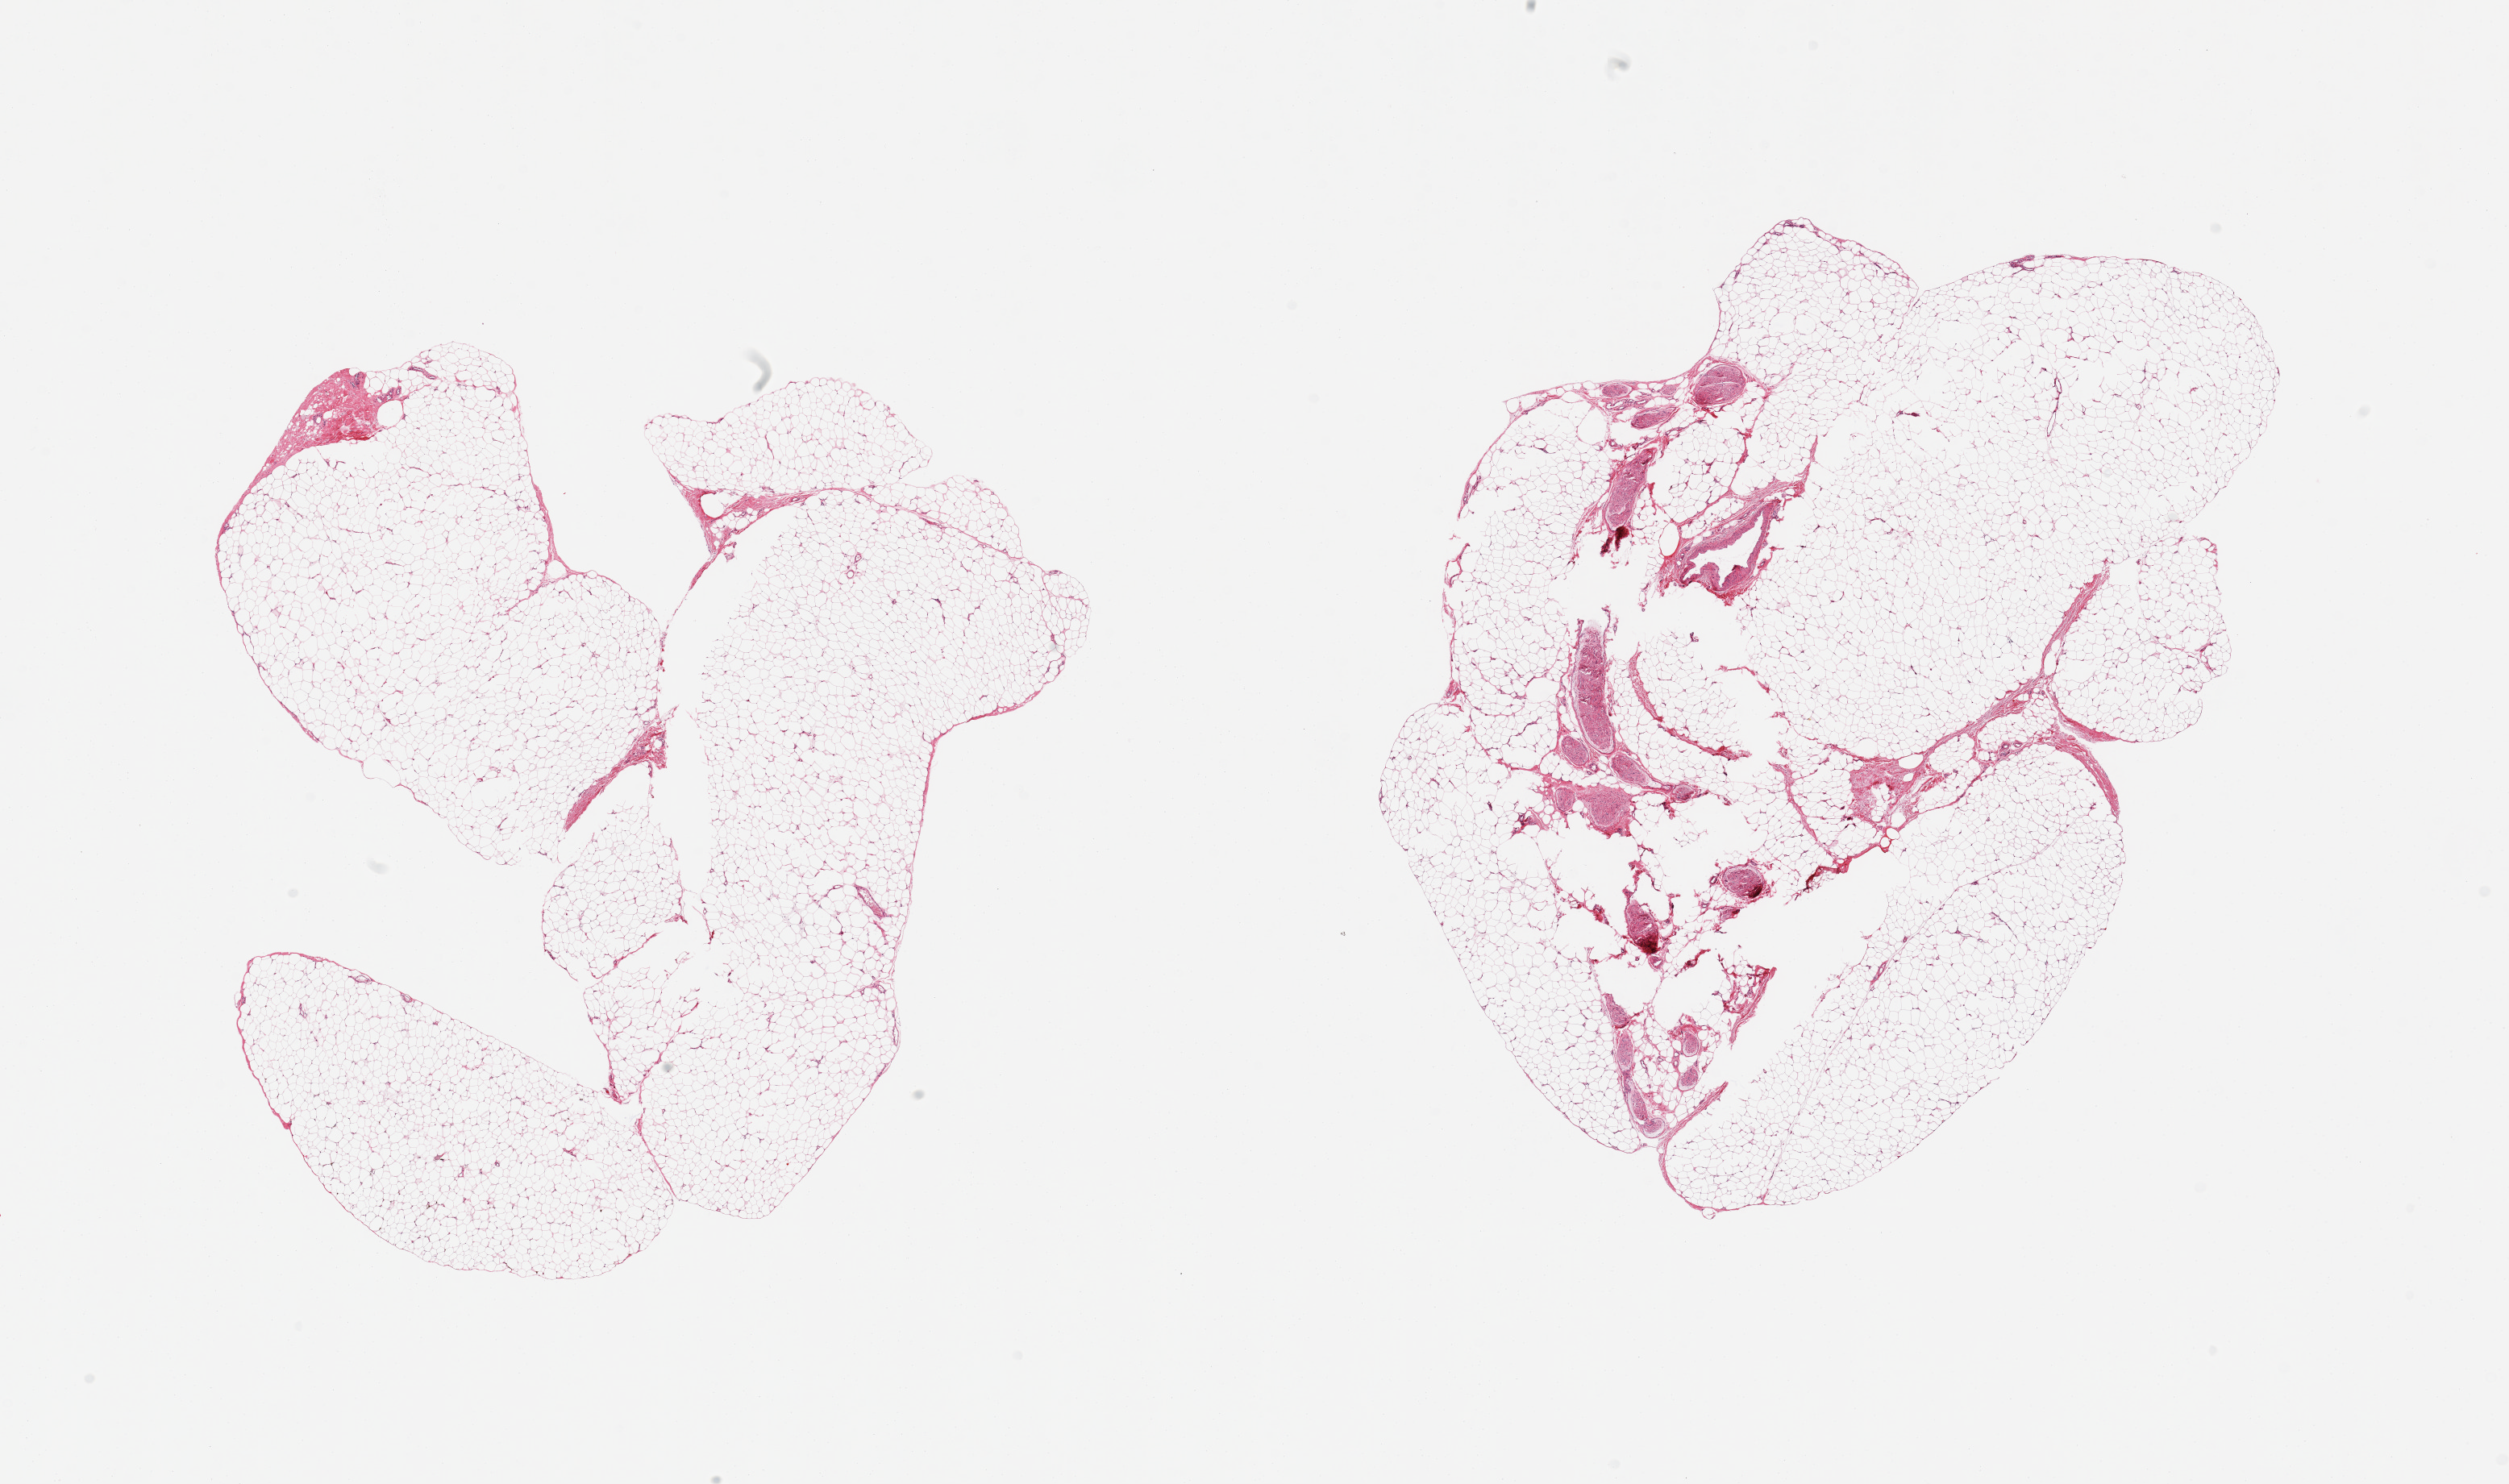
Whole-slide image, H&E stain — shown as a low-resolution overview of the whole scanned area (about 24.6 x 14.6 mm, acquisition: 20x scan); PAXgene-fixed paraffin-embedded (PFPE) section; target tissue: adipose tissue; donor tissue sample. Donor: female.
Review note (as recorded): 2 pieces: 1 with 5% neural tissue.